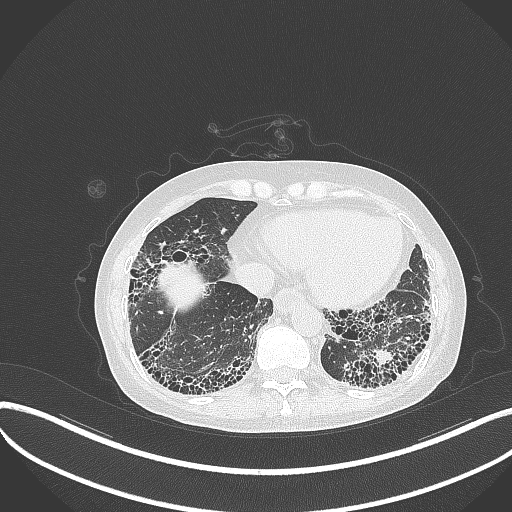
Chest CT, one axial slice; position 75 of 373 along the scan axis; reconstruction kernel B70f; 120 kVp; lung window (W 1500 / L -600 HU); 1 mm slice thickness; 512 × 512 image matrix, field of view 400 × 400 mm. Female patient, age 56 years. Case-level facts recorded for this patient, not image findings: clinical TNM (as recorded): T1 N0 M0.
Outlined on this slice (rectangle marked by the reading radiologist):
- lung tumour (recorded histology: adenocarcinoma): box from (x=365, y=346) to (x=402, y=375) px